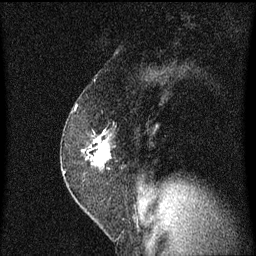
Breast MRI (dynamic contrast-enhanced), one sagittal slice. Slice 40 of 60 in the series (ordered by position). Dynamic contrast-enhanced series, image 2 of 3 at this slice position (ordered by acquisition). 1.5 T. TE 4.2 ms, TR 8.4 ms. 2 mm slice thickness. 256 × 256 image matrix, field of view 200 × 200 mm. Female patient, age 52 years. From the clinical record (not read from this slice): setting: breast cancer imaged before/during neoadjuvant chemotherapy; receptor status: HER2-positive.
Structures marked on this image (semi-automatic segmentation, software-assisted and operator-edited):
- analysis volume of interest (the breast-tissue region the enhancement analysis was run in; not a lesion): bounding box <62,124,116,191> (left, top, right, bottom; pixels)
- tumour enhancement mask (voxels above the 70 % enhancement threshold inside the analysis volume of interest): <91,130,109,167>